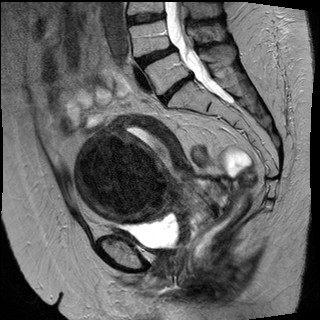
Pelvic MRI for cervical cancer, one sagittal slice; T2-weighted; 1.5 T; TE 89 ms, TR 4880 ms; 320 × 320 image matrix. Female patient, age 50 years.
Structures marked on this image (outlined manually by an expert reader):
- uterus and cervix: bounding box (x1, y1, x2, y2) in pixels: (75, 115, 235, 248)